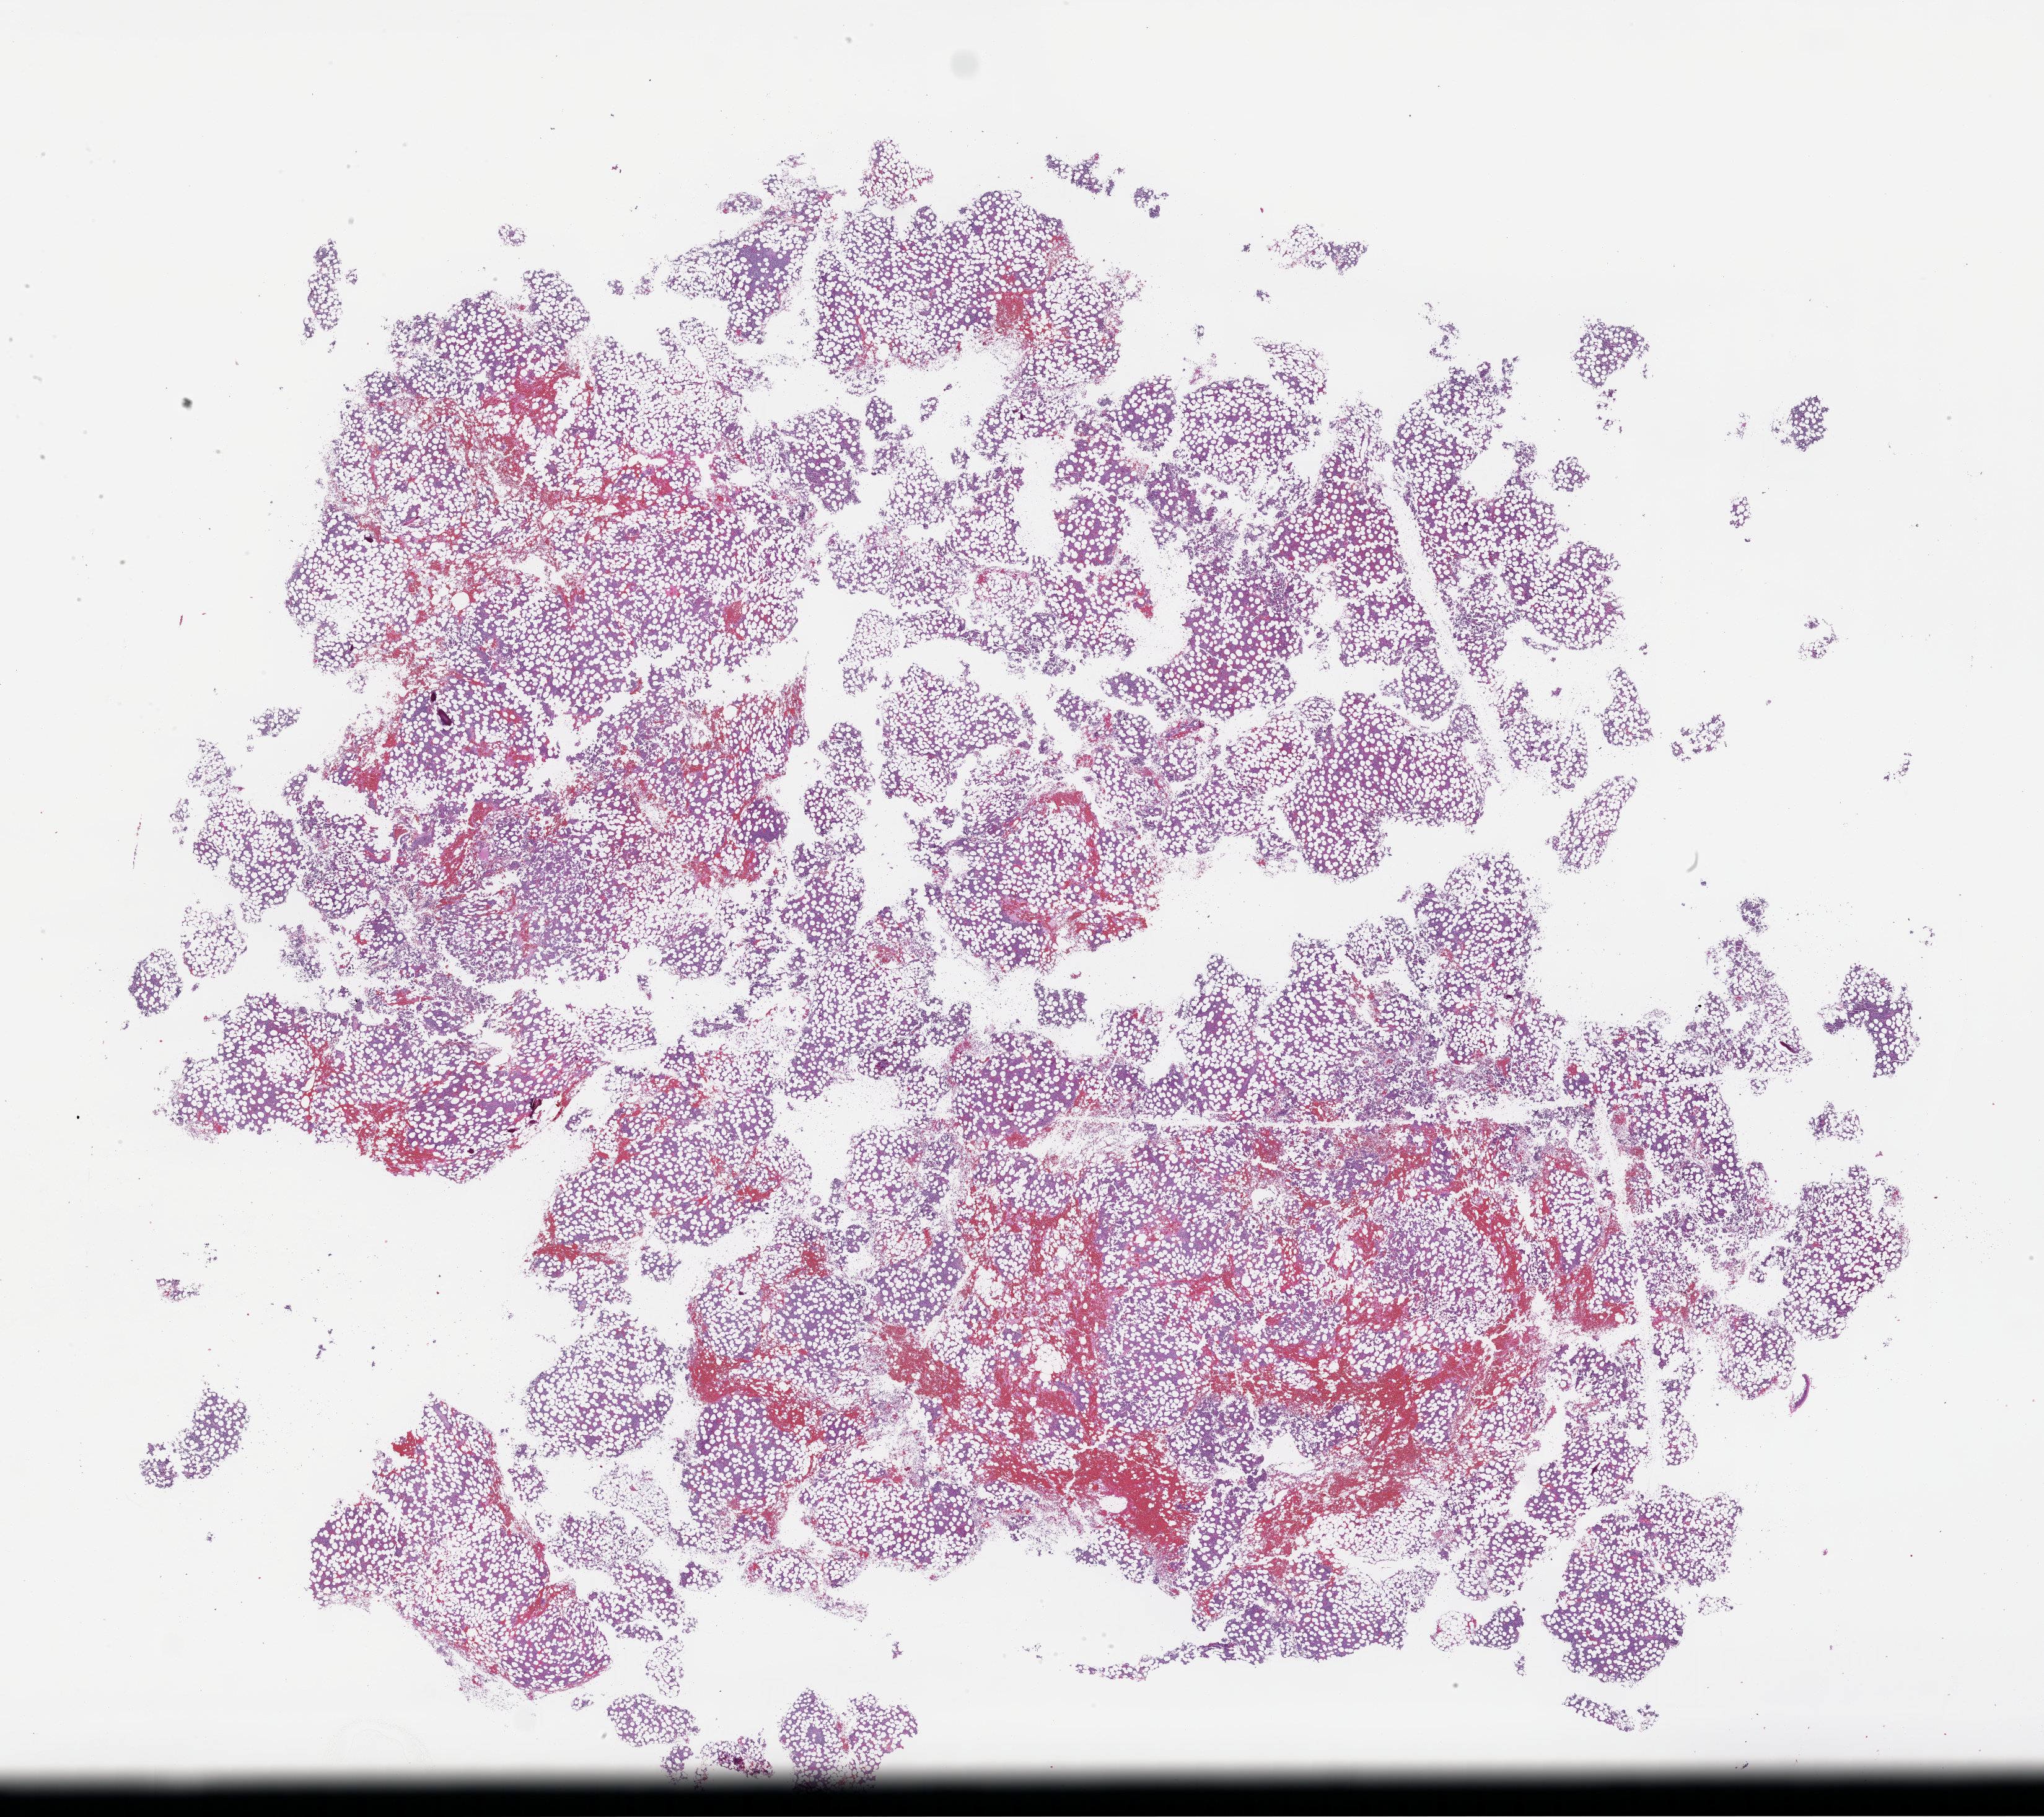
Whole-slide image, H&E stain — shown as a low-resolution overview of the whole scanned area (about 26.6 x 23.7 mm). Formalin-fixed, paraffin-embedded (FFPE) tissue. Site: bone marrow. Archival tissue. Male patient.
This section: primary tumor. Diagnosis: Plasma Cell Myeloma.